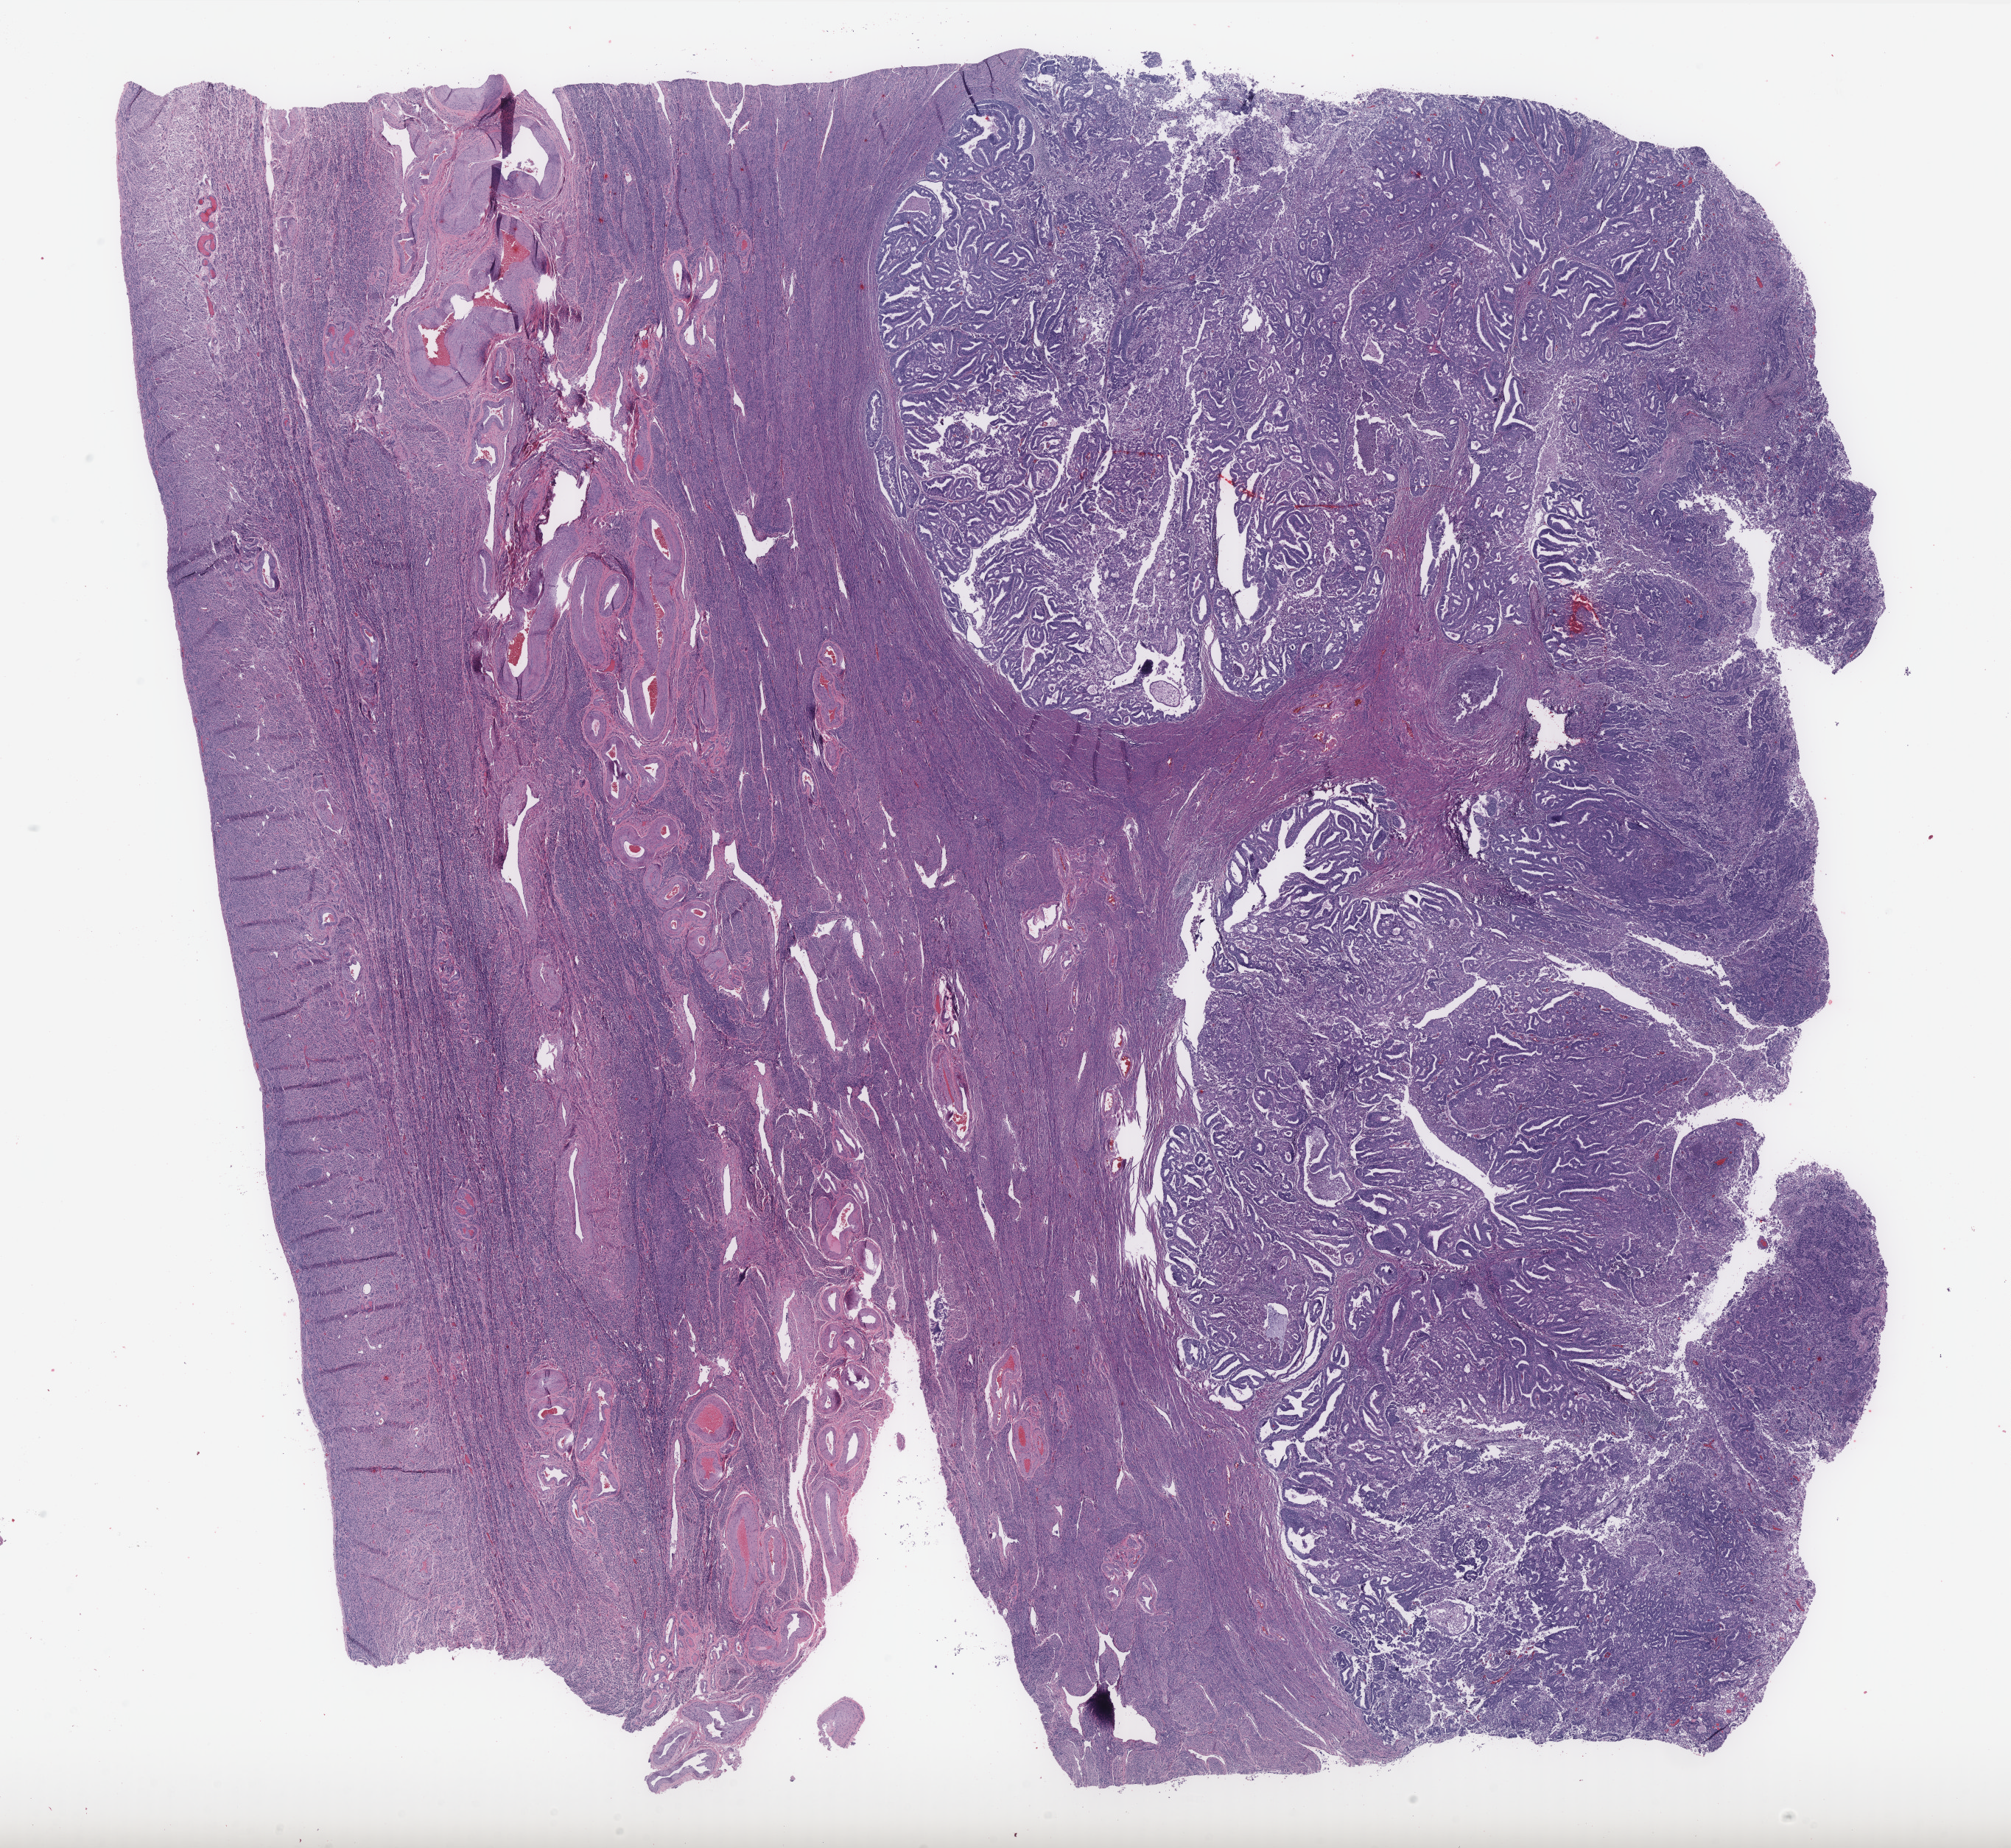
Digitized H&E tissue section (whole slide) — low-resolution overview of the scanned area, about 21.9 x 20.1 mm (slide scanned at 40x), FFPE section, uterus, primary tumour sample. Patient: female, age at initial diagnosis 62 years. Histologic grade: G2 (moderately differentiated).
Diagnosis: Endometrioid adenocarcinoma, NOS (endometrium). FIGO stage: IB. Lymph nodes positive (case pathology): 0 of 1 examined.